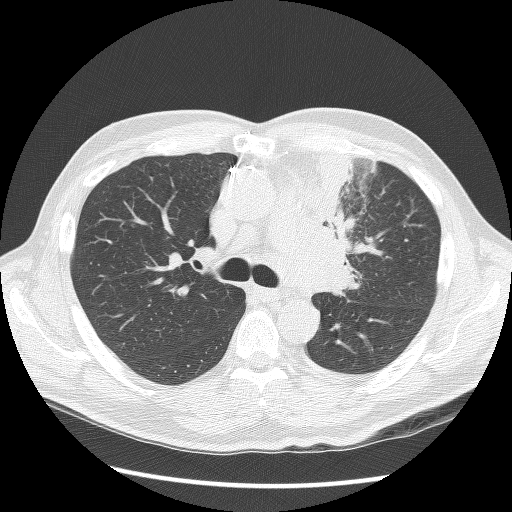
Chest CT (low-dose screening protocol), one axial image, second screening round (one year after baseline), lung window (W 1500 / L -600 HU), 2.5 mm slice thickness, slice 46 of 136 in the series. Male participant, aged 64 years at enrolment. Former smoker at enrolment.
- Lesion marked by an expert reader, bounding box (x1, y1, x2, y2) in pixels: (300, 155, 377, 286).
- No non-calcified nodule or mass ≥4 mm was recorded by the screening reader at this exam.
- Participant outcome: lung cancer diagnosed 24 days after this screen — small cell carcinoma, NOS, left upper lobe, stage IV (AJCC 6th edition), 100 mm at pathology.